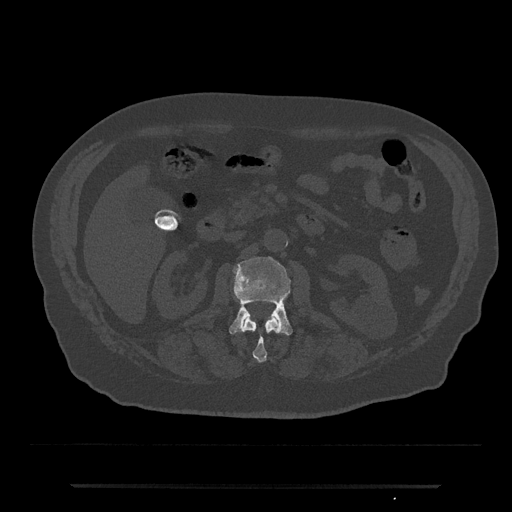
CT including the spine, one axial slice. Slice 497 of 797 in the series (ordered by position). Bone window (W 1800 / L 400 HU). 512 × 512 image matrix. Patient: male, 80 years. From the clinical record (not read from this slice): primary cancer: prostate; vertebrae with lytic lesions (as recorded): L1, T11.
Outlined on this slice (semi-automatically segmented with operator editing):
- L1 vertebra: bounding box <243,317,281,363> (left, top, right, bottom; pixels)
- L2 vertebra: <229,257,293,335>